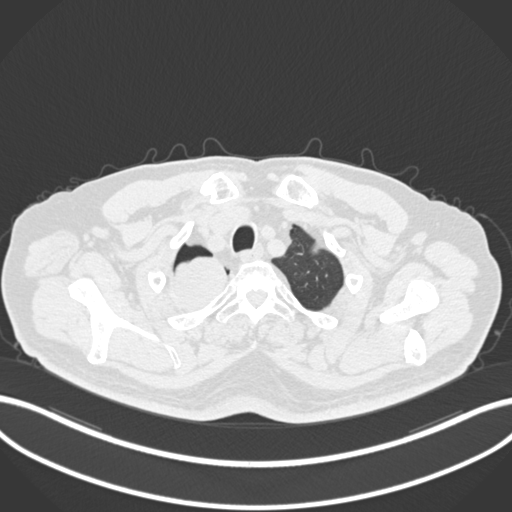
Chest CT, one axial slice. Position 194 of 218 along the scan axis. Reconstruction kernel B30f. Lung window (W 1500 / L -600 HU). 1 mm slice thickness. 512 × 512 image matrix. Patient: male, 68 years. From the clinical record (not read from this slice): clinical TNM (as recorded): T2a N0 M0.
Annotated regions visible in this slice (rectangle marked by the reading radiologist):
- lung tumour (recorded histology: adenocarcinoma): box from (x=169, y=249) to (x=230, y=317) px